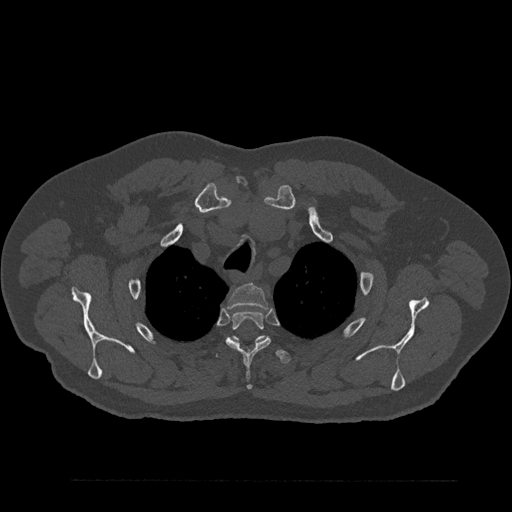
CT including the spine, one axial slice. Slice 682 of 797 in the series (ordered by position). Reconstruction kernel Br40s/3. 120 kVp. Bone window (W 1800 / L 400 HU). 0.5 mm slice thickness. 512 × 512 image matrix, field of view 430 × 430 mm. Male patient, age 61 years. From the clinical record (not read from this slice): primary cancer: prostate.
Structures marked on this image (semi-automatic segmentation, software-assisted and operator-edited):
- T2 vertebra: box from (x=227, y=284) to (x=268, y=309) px
- T3 vertebra: (x=225, y=311)–(x=271, y=390)
- T4 vertebra: (x=208, y=336)–(x=291, y=364)